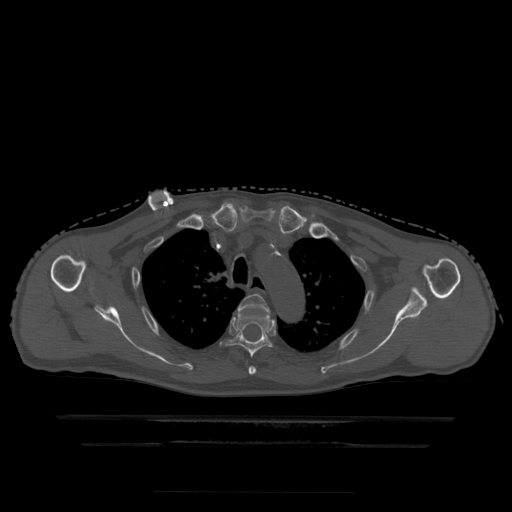
CT including the spine, one axial slice. Slice 358 of 522 in the series (ordered by position). Bone window (W 1800 / L 400 HU). 1.25 mm slice thickness. 512 × 512 image matrix, field of view 436 × 436 mm. Patient age 68 years. From the clinical record (not read from this slice): primary cancer: urothelial.
Structures marked on this image (semi-automatic segmentation, software-assisted and operator-edited):
- T3 vertebra: bounding box [x1, y1, x2, y2] px = [238, 294, 270, 375]
- T4 vertebra: [222, 311, 273, 358]